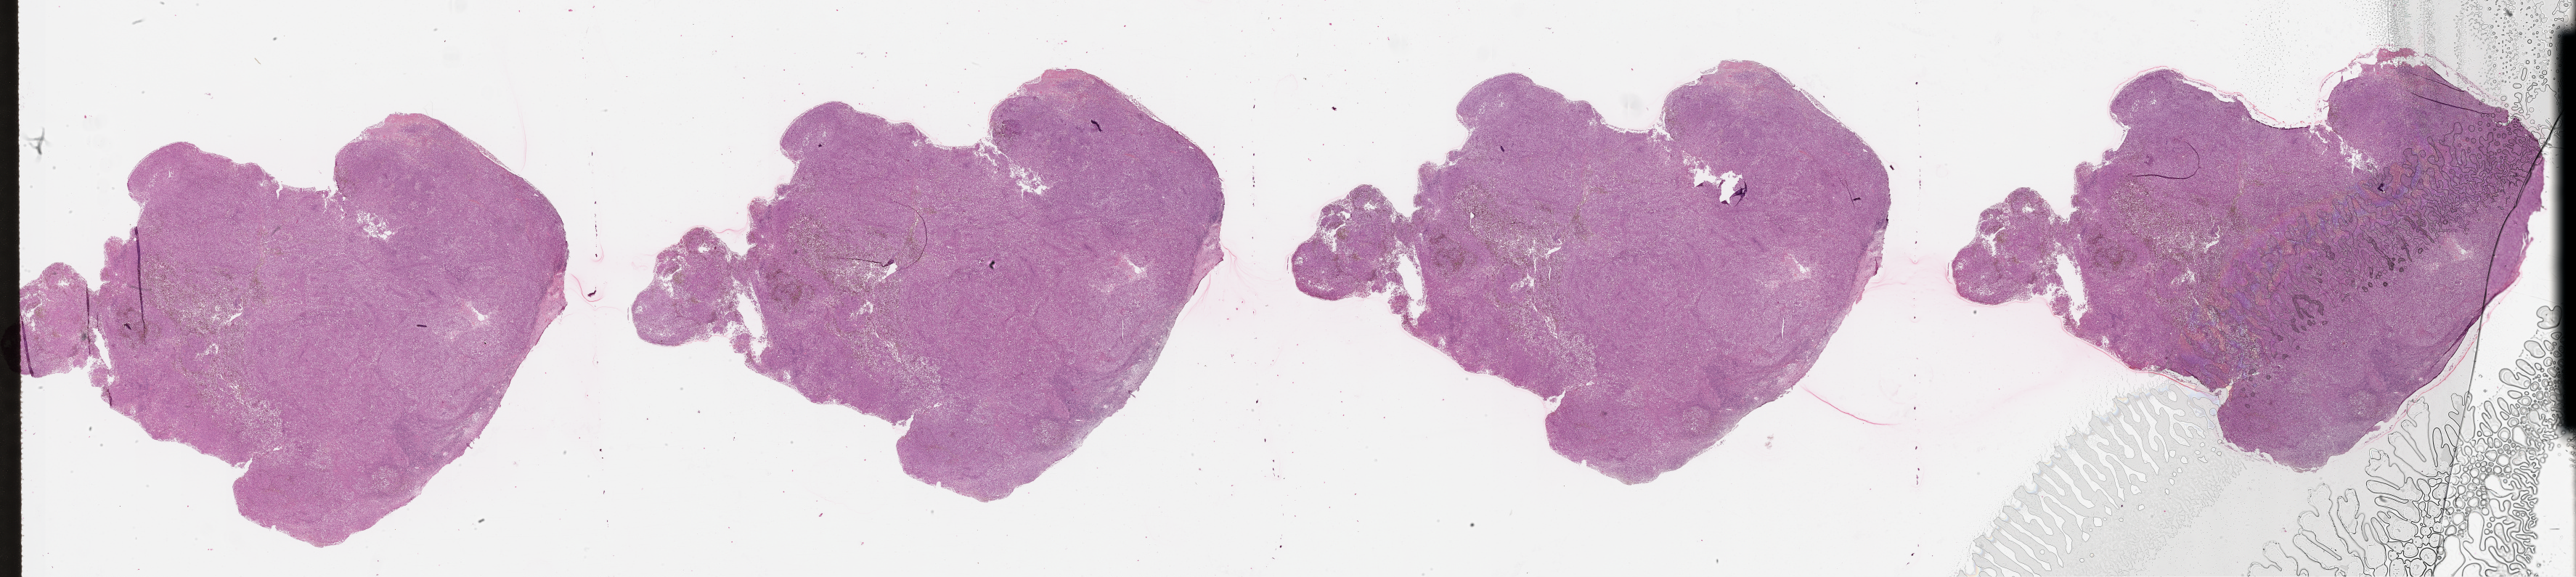
H&E whole-slide image, low-resolution overview of the scanned area, about 57.1 x 12.8 mm (from a 20x scan), tumour tissue sample, sampled site: lymph node. Male, 87 y/o. Pathologist review of this section (percent, as recorded): tumour nuclei 90%, necrosis 0%.
This section: metastatic tumour tissue. Patient diagnosis: Malignant melanoma, NOS.